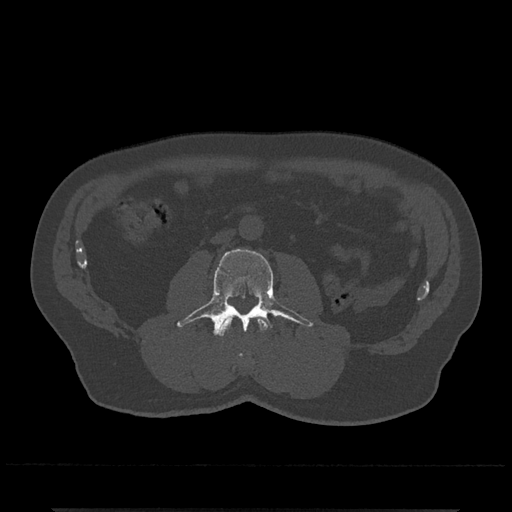
CT including the spine, one axial slice; slice 231 of 797 in the series (ordered by position); 120 kVp; bone window (W 1800 / L 400 HU); 0.5 mm slice thickness; 512 × 512 image matrix, field of view 393 × 393 mm. Male patient, age 67 years. From the clinical record (not read from this slice): primary cancer: prostate.
Annotated regions visible in this slice (semi-automatic segmentation, software-assisted and operator-edited):
- L2 vertebra: box from (x=218, y=316) to (x=269, y=358) px
- L3 vertebra: (x=177, y=249)–(x=313, y=337)